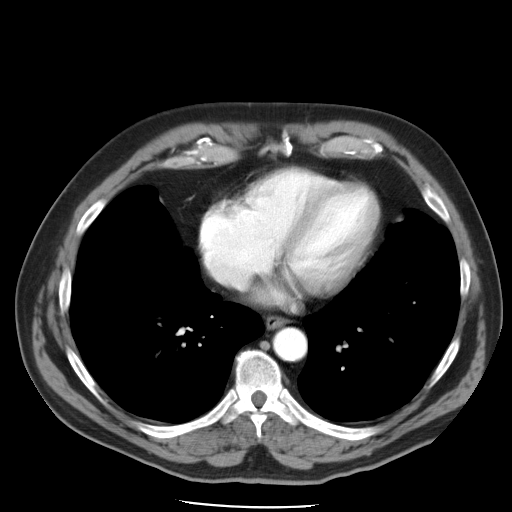
Contrast-enhanced abdominal CT, one axial slice; intravenous contrast given; soft-tissue window (W 400 / L 40 HU); 5 mm slice thickness; 512 × 512 image matrix, field of view 395 × 395 mm. Male patient, age 68 years. From the clinical record (not read from this slice): diagnosis: colorectal cancer liver metastases, imaged before liver resection; multiple liver metastases: yes; largest metastasis: 1.7 cm; chemotherapy before resection: yes.
Structures marked on this image (expert manual segmentation):
- hepatic veins: bounding box (x1, y1, x2, y2) in pixels: (216, 273, 253, 290)